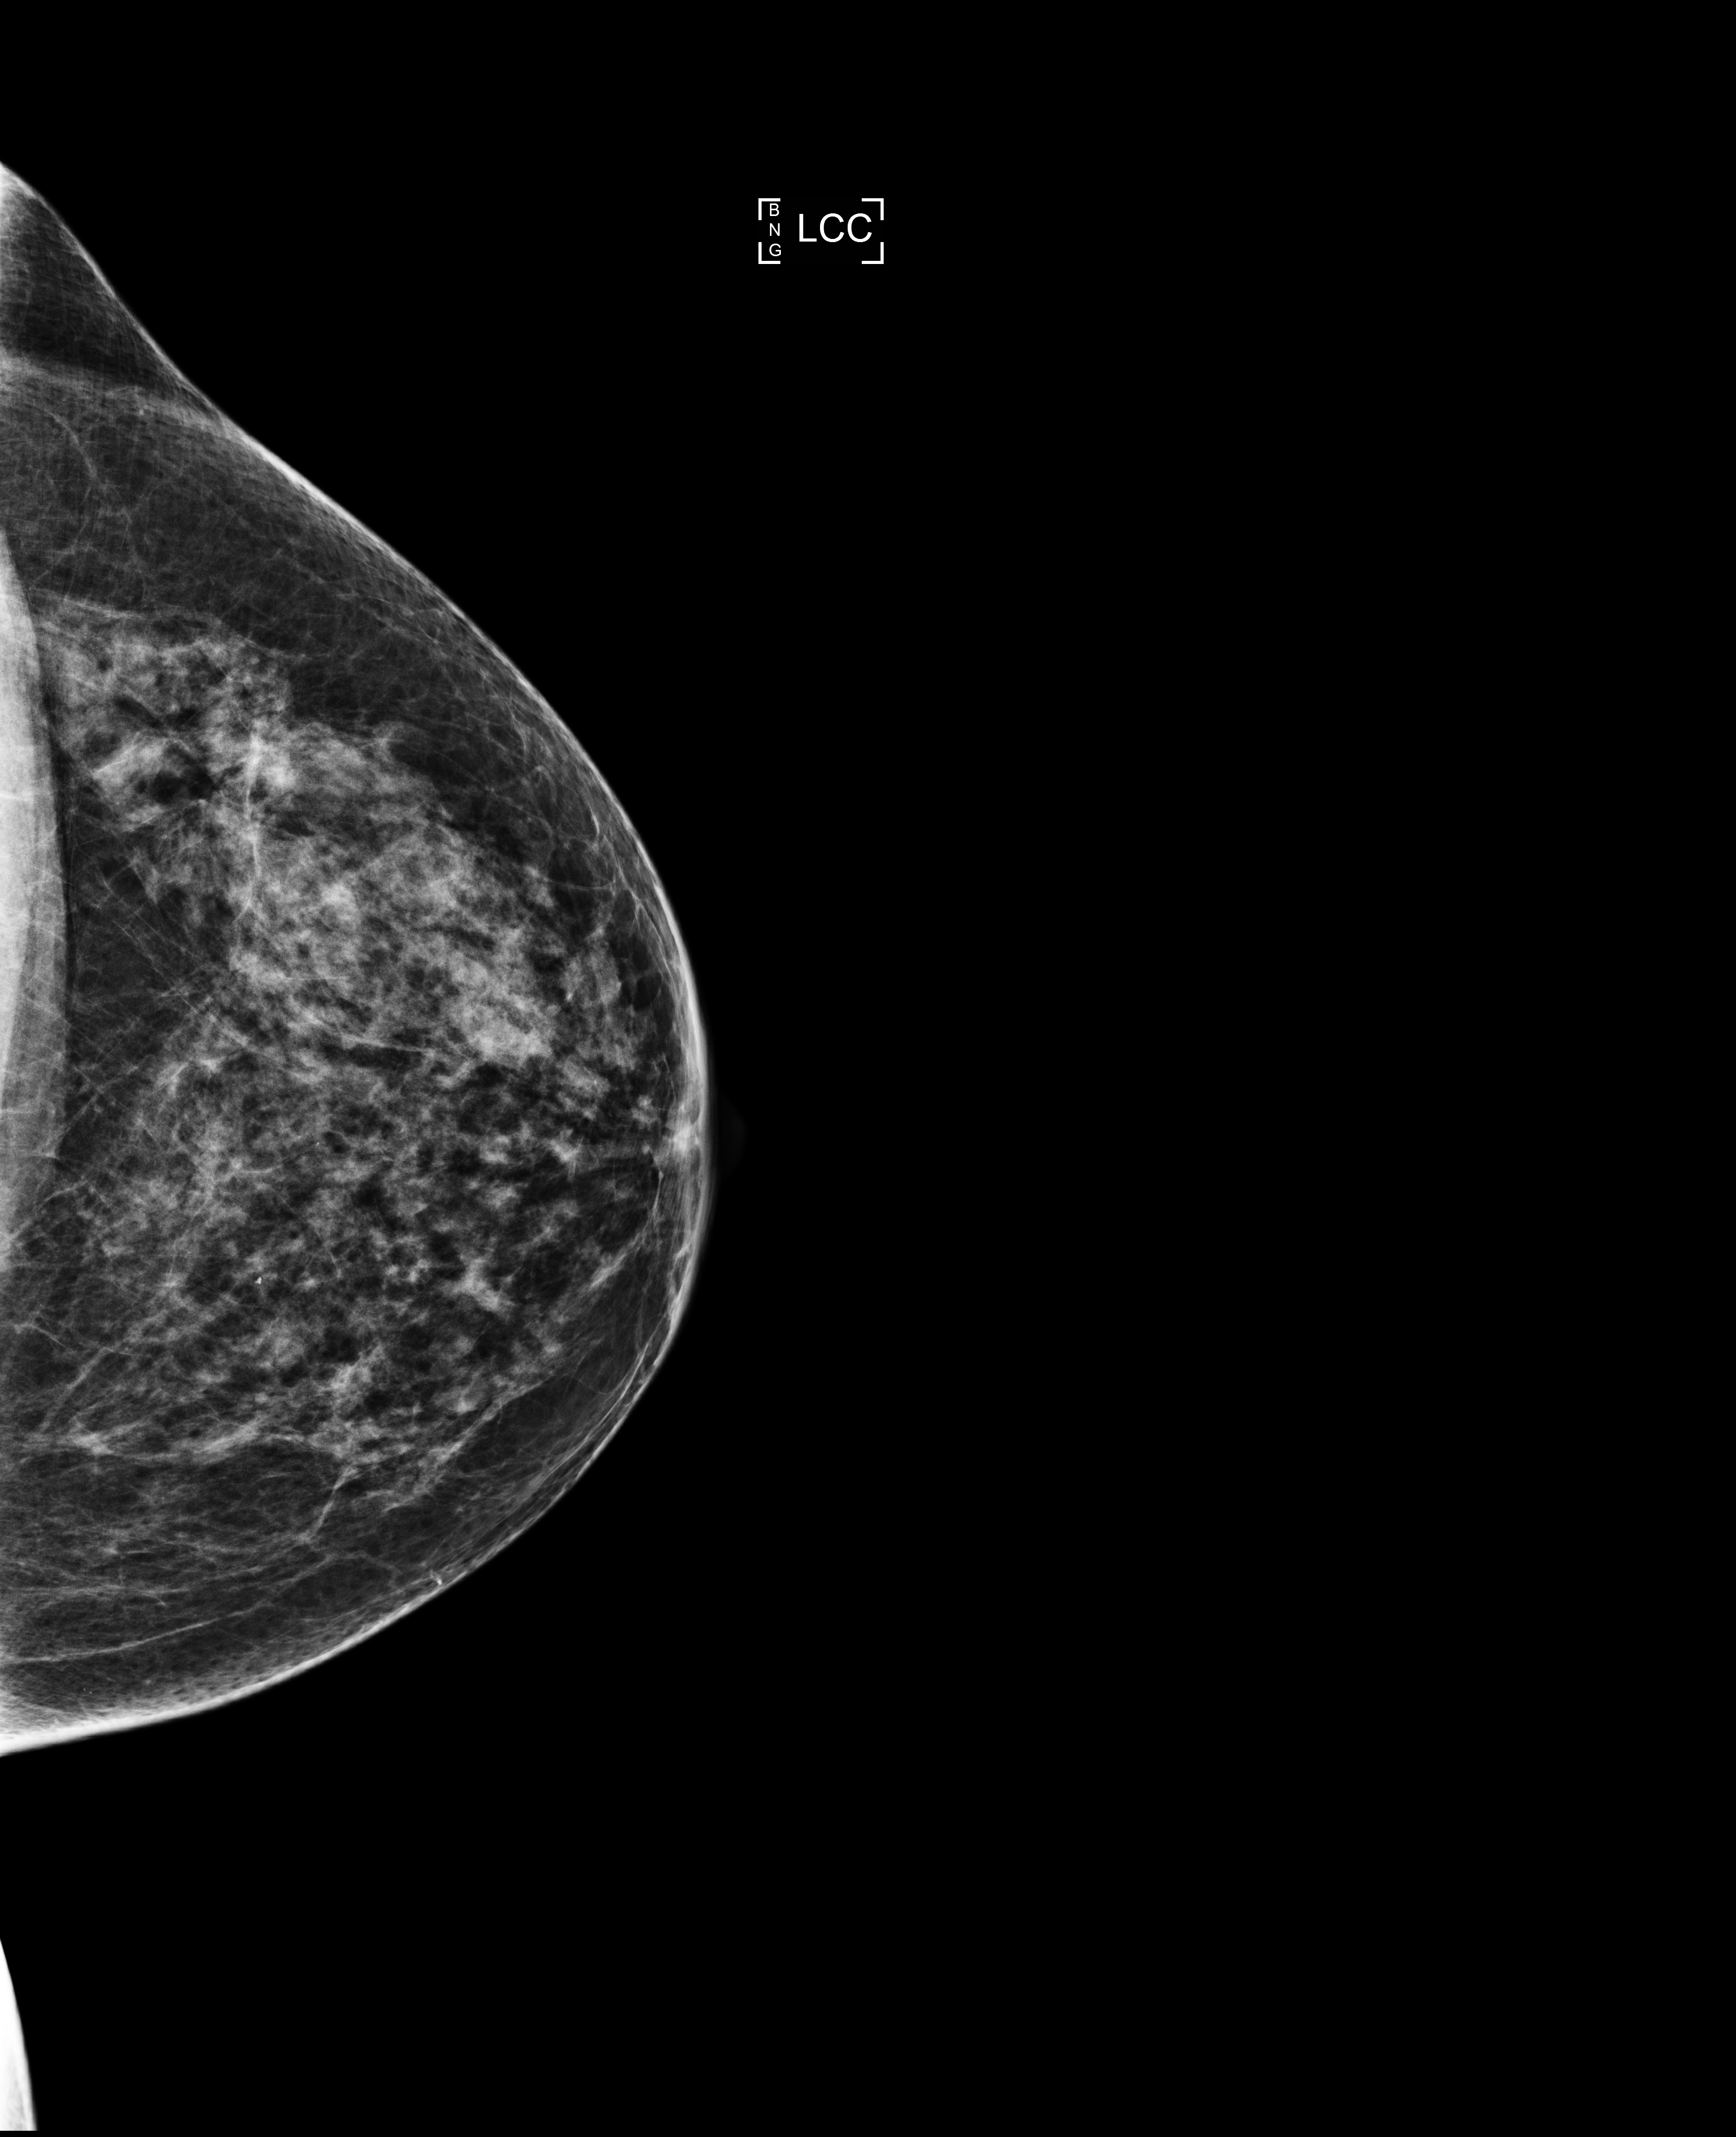
Screening examination; compressed breast thickness 67 mm; system: Selenia Dimensions. Patient: female, 62 years.
Image type: full-field digital mammogram. Breast: left. Projection: craniocaudal (CC) view.